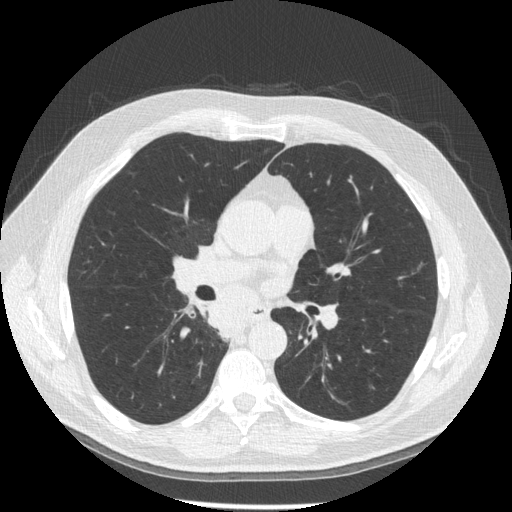
Axial slice from a low-dose chest CT screening exam; third annual screen; lung window (W 1500 / L -600 HU); slice 82 of 181 in the series. Male, age 61 years at enrolment.
• Expert reader's lesion annotation, bounding box <205,298,255,346> (left, top, right, bottom; pixels).
• Screening reader's record for this exam: no non-calcified nodule ≥4 mm recorded.
• Official screen result: positive, other.
• Later outcome: lung cancer diagnosed 10 days after this screen — squamous cell carcinoma, keratinizing, NOS, right lower lobe, stage IIIB (AJCC 6th edition), 40 mm at pathology.